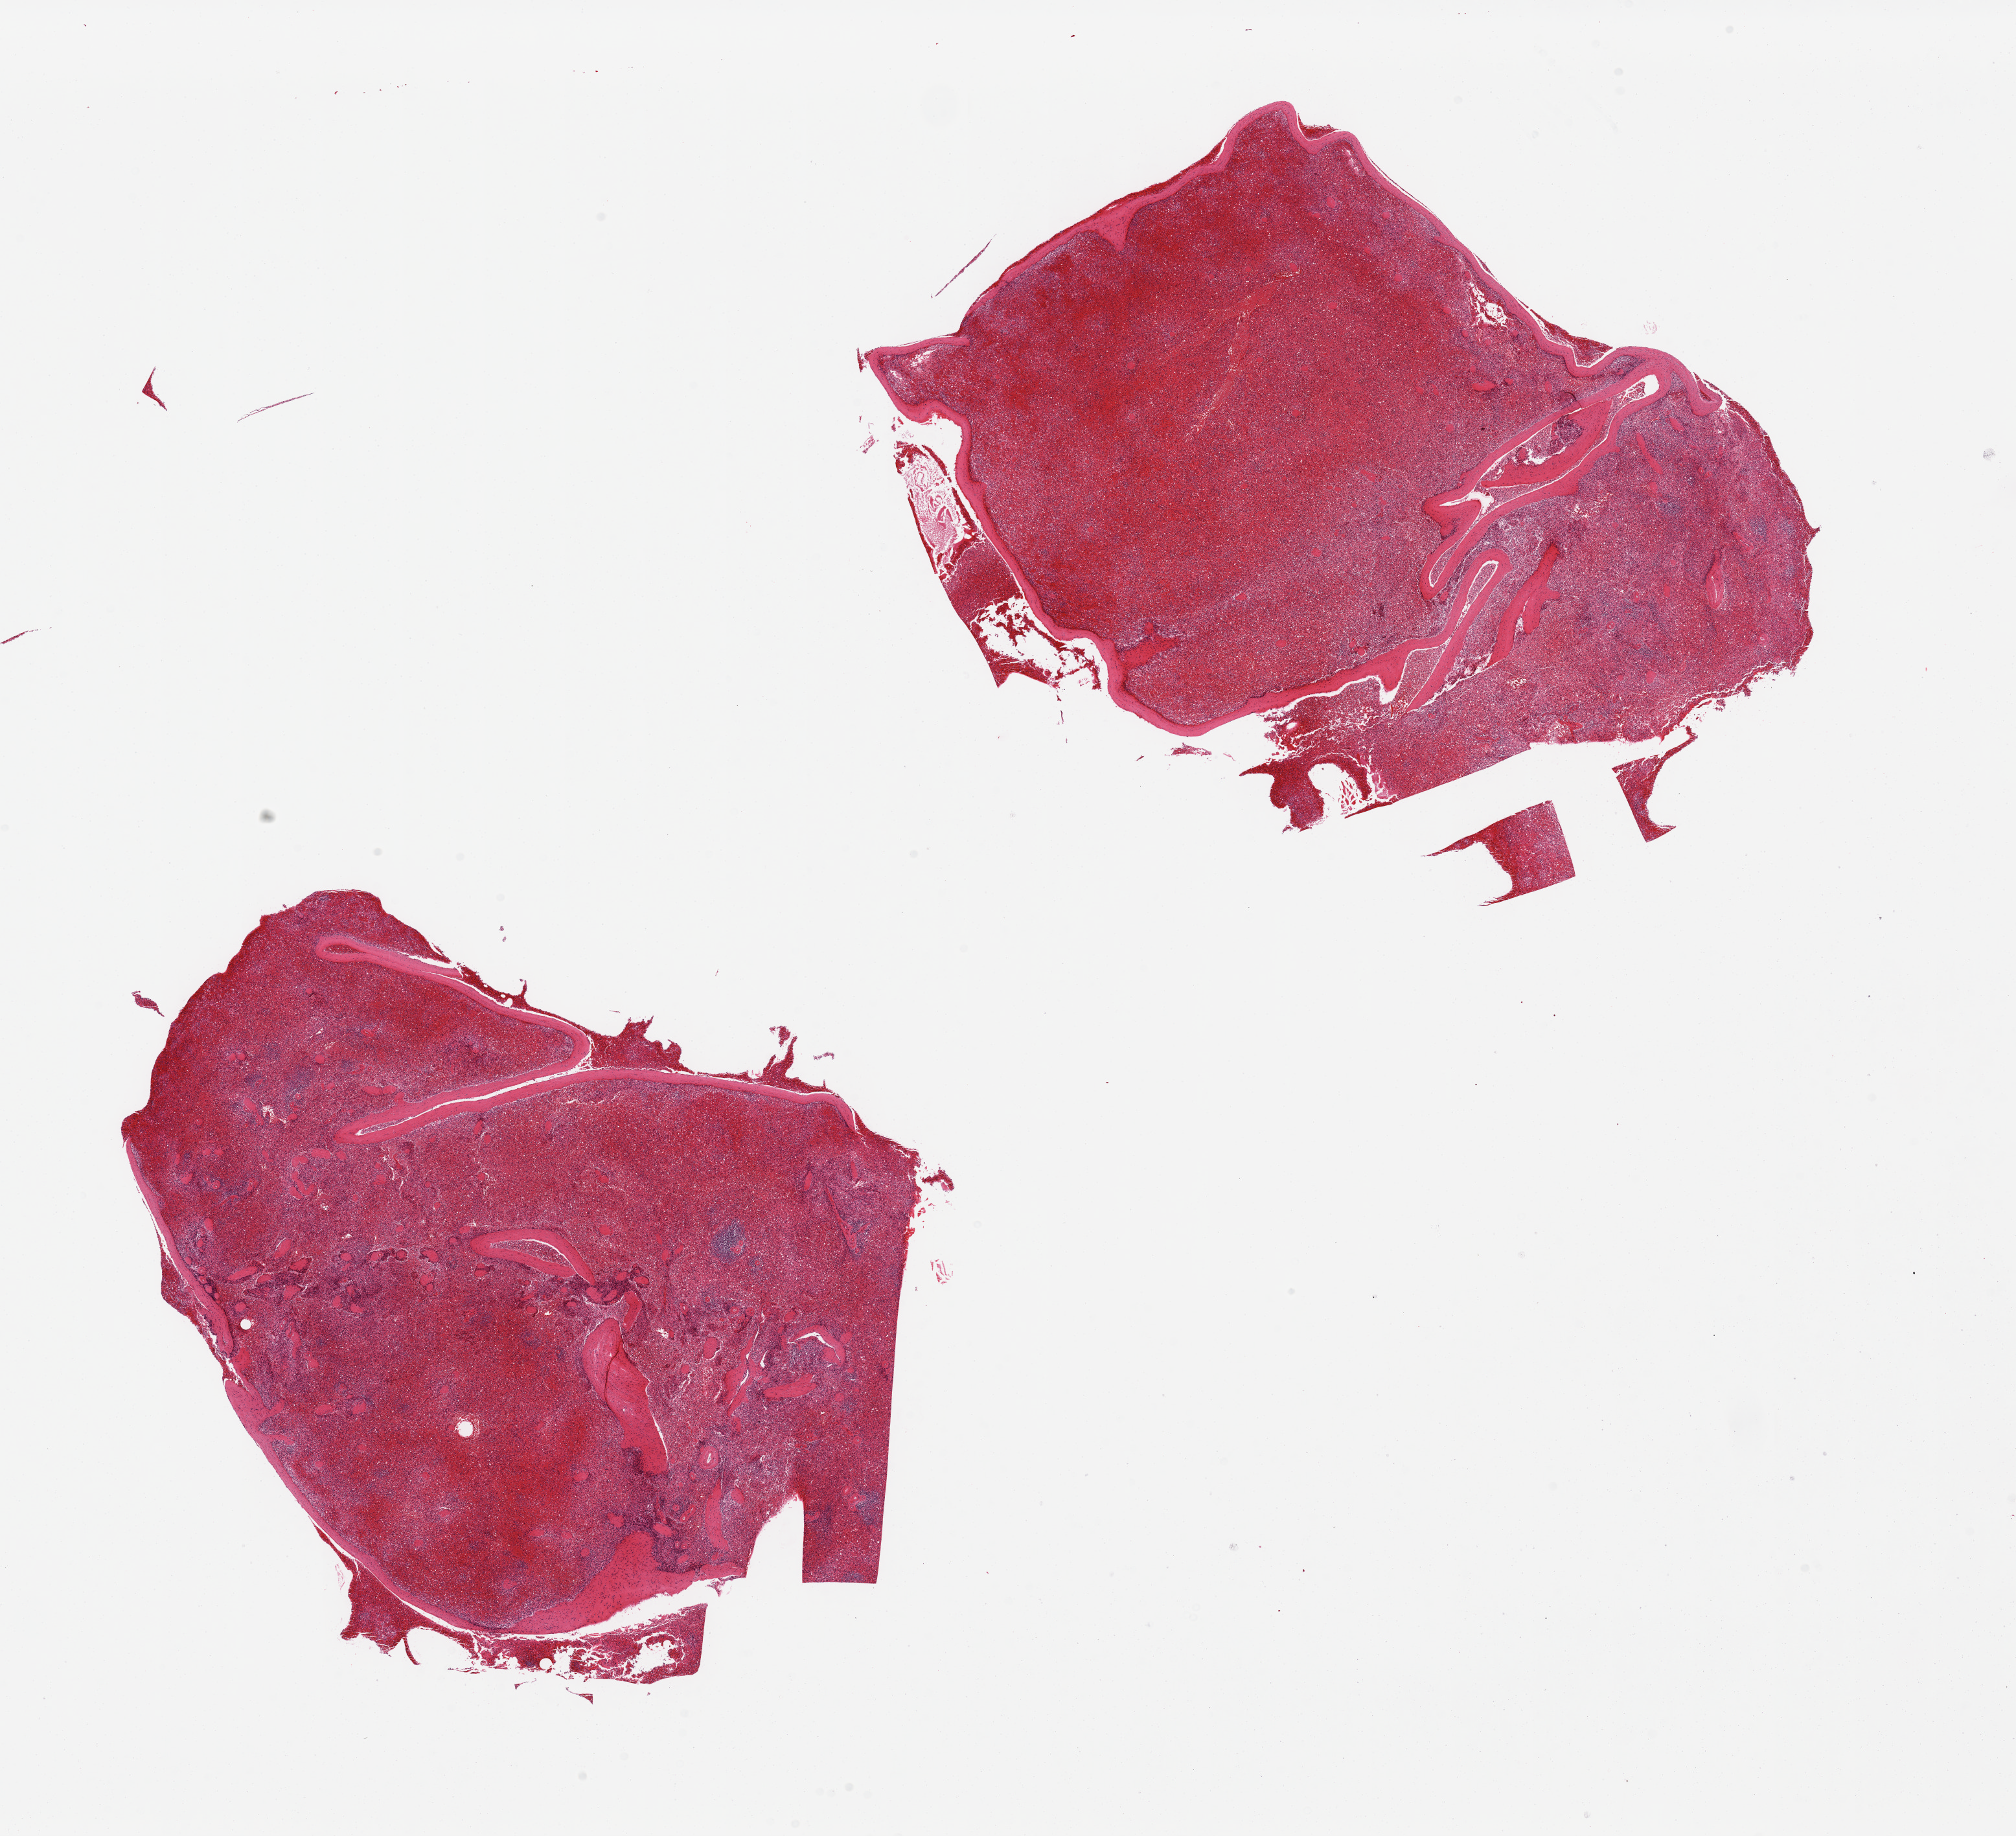
Whole-slide image, haematoxylin and eosin stain, shown as a low-resolution overview of the whole scanned area (about 24.6 x 22.4 mm, acquisition: 20x scan). PAXgene-fixed paraffin-embedded (PFPE) section. Target tissue: spleen. Tissue donor sample. Male donor.
Review note (as recorded): 2 pieces, includes capsule (target is 1 cm below capsule), congested.